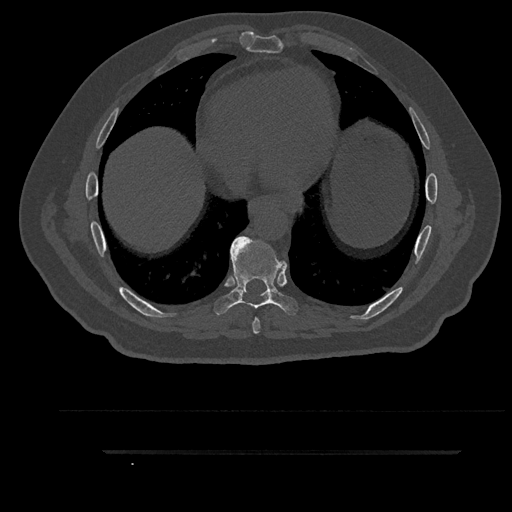
CT including the spine, one axial slice; reconstruction kernel Br40s/3; bone window (W 1800 / L 400 HU); 512 × 512 image matrix, field of view 432 × 432 mm. Patient: male, 63 years. From the clinical record (not read from this slice): primary cancer: renal; vertebrae with lytic lesions (as recorded): T8.
Annotated regions visible in this slice (semi-automatically segmented with operator editing):
- T7 vertebra: bounding box [x1, y1, x2, y2] px = [252, 317, 261, 334]
- T8 vertebra: [214, 236, 298, 315]